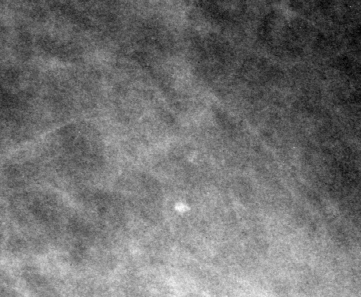
Cropped region of a digitized screen-film mammogram centred on a radiologist-marked abnormality, left breast, MLO view, BI-RADS breast density category 3 (scale 1–4).
Finding: calcifications, morphology punctate, distribution segmental; BI-RADS assessment category 2; benign without callback (not worked up further).